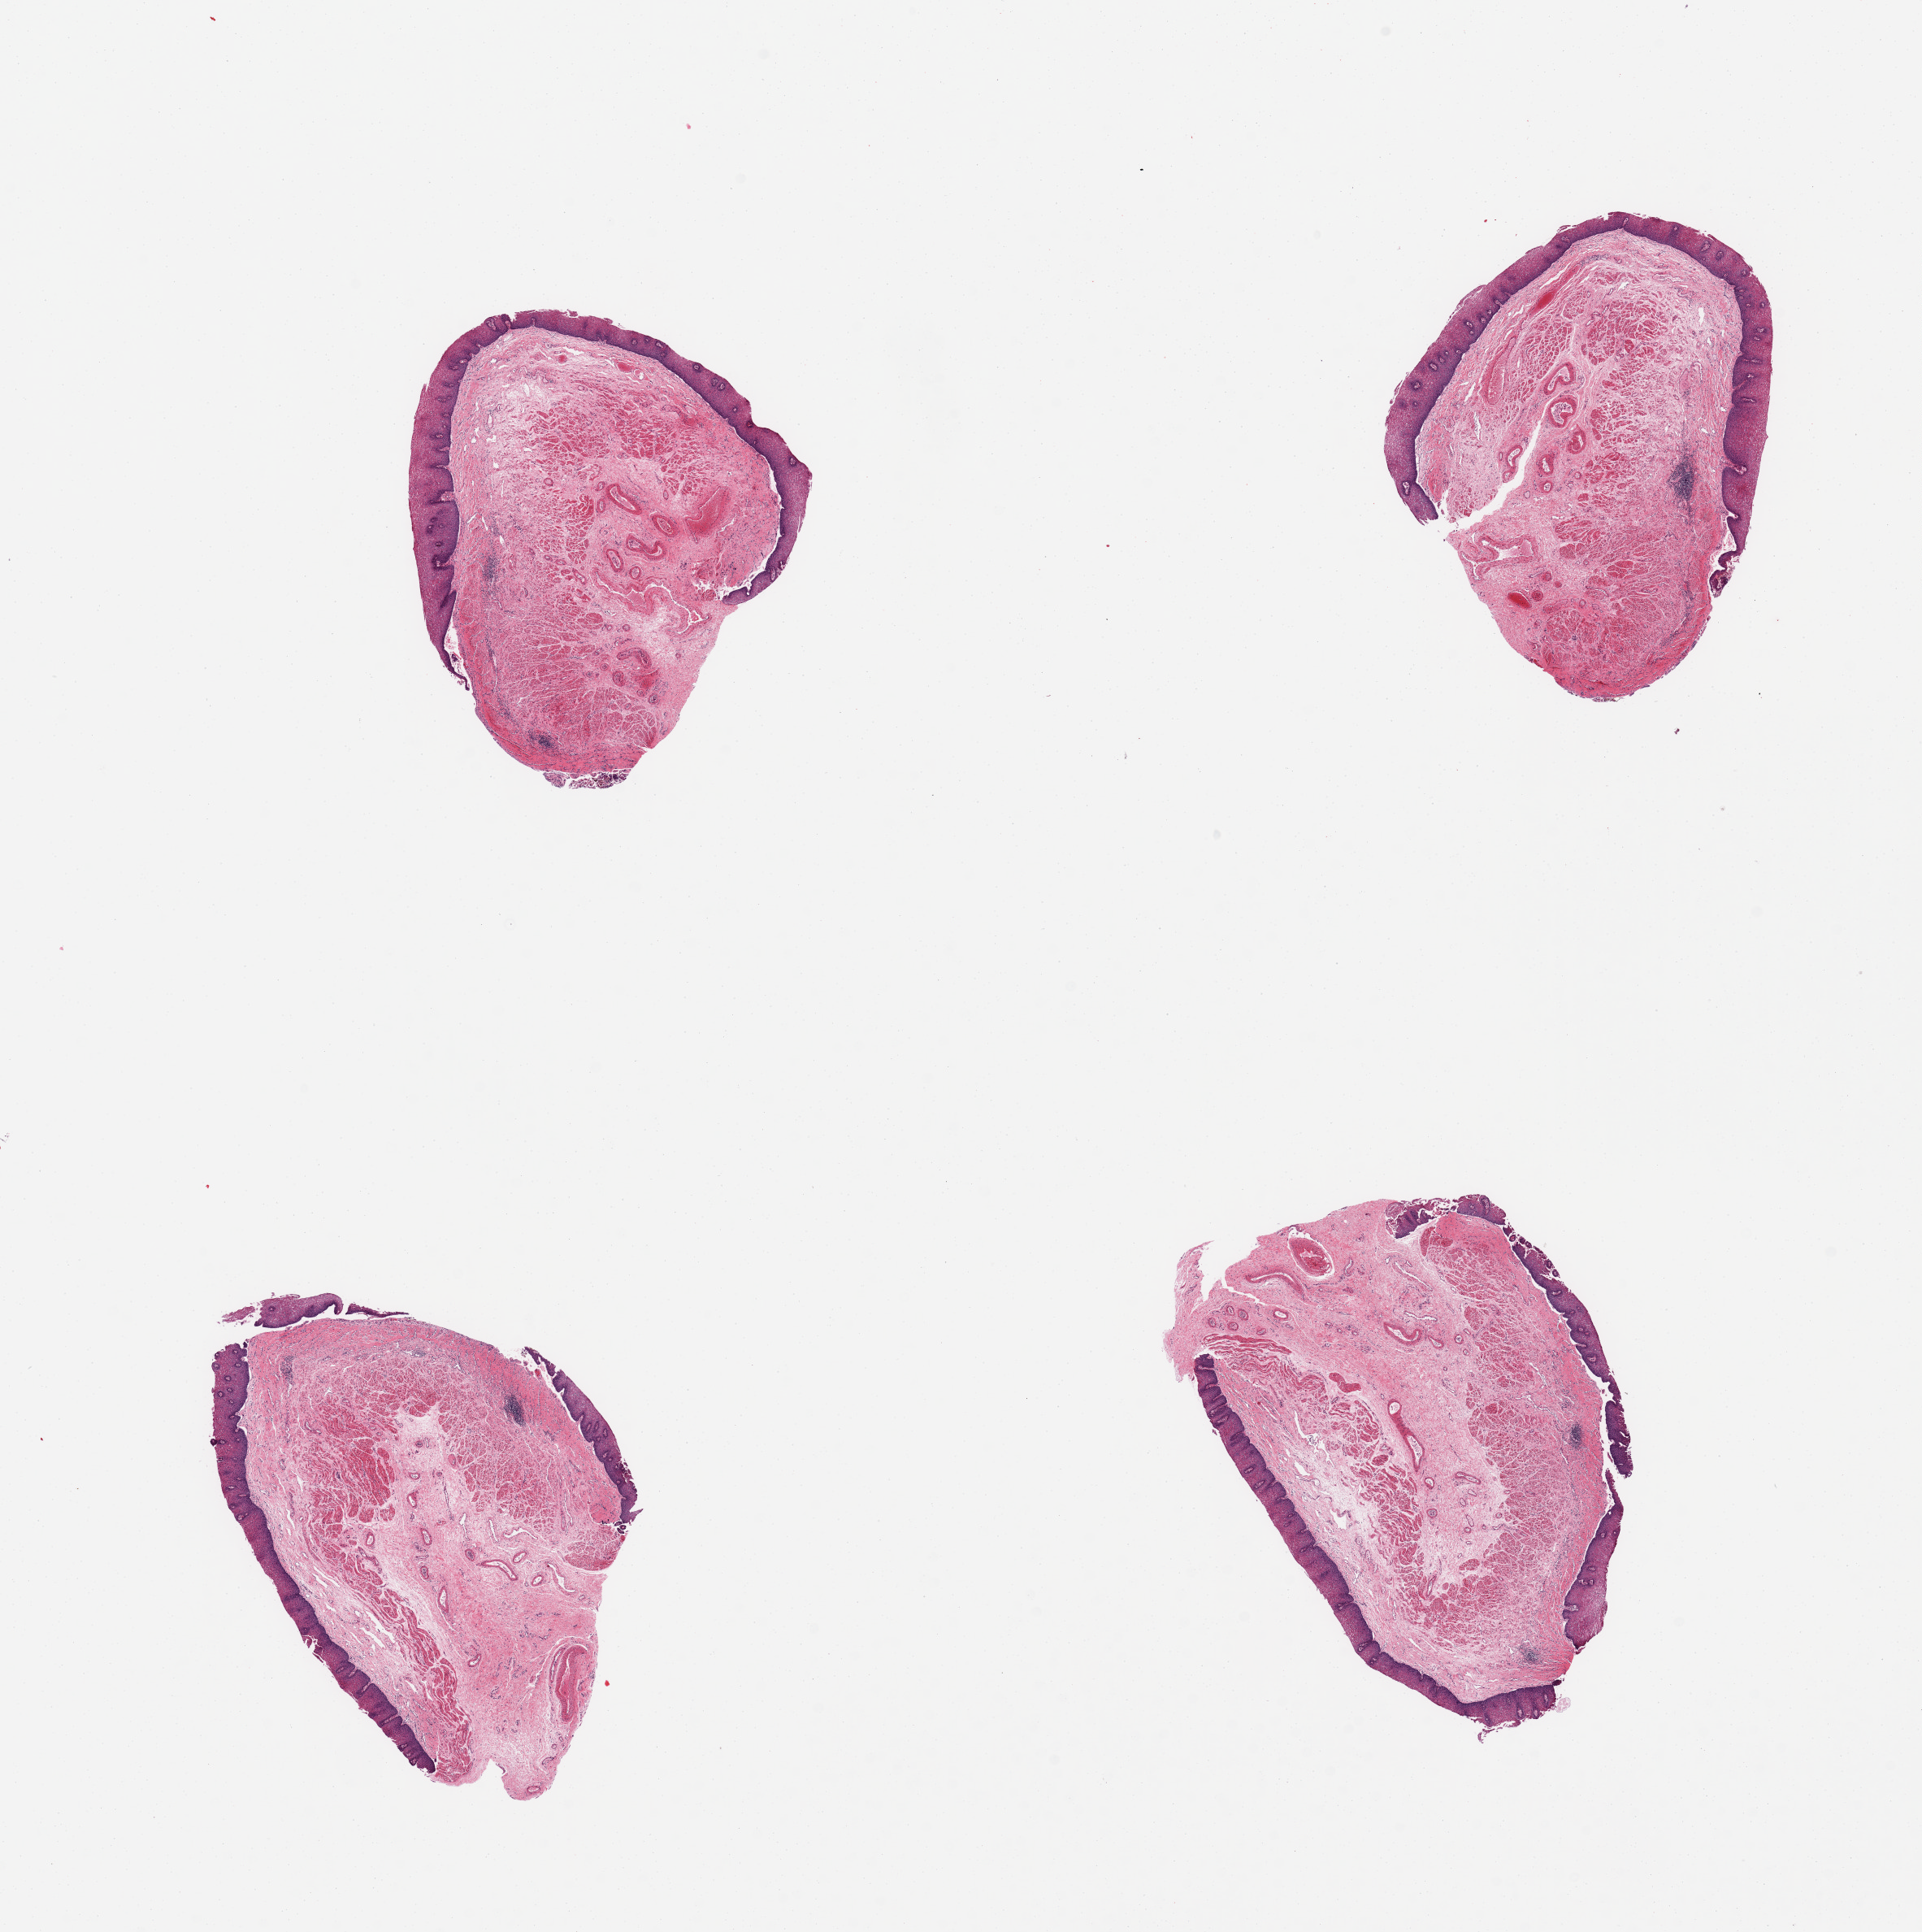
Haematoxylin and eosin whole-slide image, brightfield, whole scanned area (about 18.7 x 18.8 mm) shown as a low-resolution overview, PAXgene-fixed paraffin-embedded (PFPE) section, target tissue: esophageal mucous membrane, donor tissue sample. Male donor.
Pathologist's review note for this sample: 4 pieces, squamous mucosa well preserved, ~0.4mm.